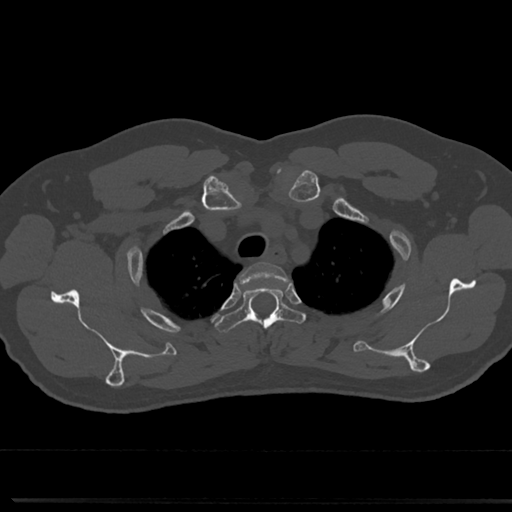
CT including the spine, one axial slice. Slice 603 of 817 in the series (ordered by position). Reconstruction kernel Br40s/3. 120 kVp. Bone window (W 1800 / L 400 HU). 0.5 mm slice thickness. 512 × 512 image matrix, field of view 355 × 355 mm. Male patient, age 61 years. From the clinical record (not read from this slice): primary cancer: prostate.
Structures marked on this image (semi-automatically segmented with operator editing):
- T2 vertebra: bounding box <245,263,284,279> (left, top, right, bottom; pixels)
- T3 vertebra: <218,280,299,337>